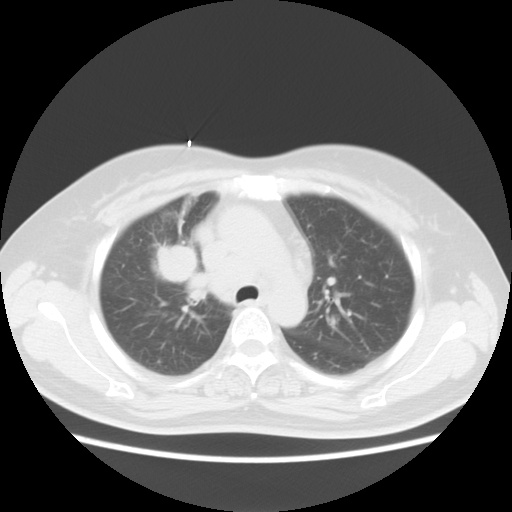
Chest CT, one axial slice; slice 10 of 18 in the series (ordered by position); reconstruction kernel STANDARD; 120 kVp; lung window (W 1500 / L -600 HU); 5 mm slice thickness; 512 × 512 image matrix, field of view 350 × 350 mm. Female patient, age 54 years. From the clinical record (not read from this slice): clinical TNM (as recorded): T2 N3 M0; histopathological grade: G3.
Outlined on this slice (bounding box drawn by a radiologist):
- lung tumour (recorded histology: small cell carcinoma): bounding box <151,236,201,291> (left, top, right, bottom; pixels)